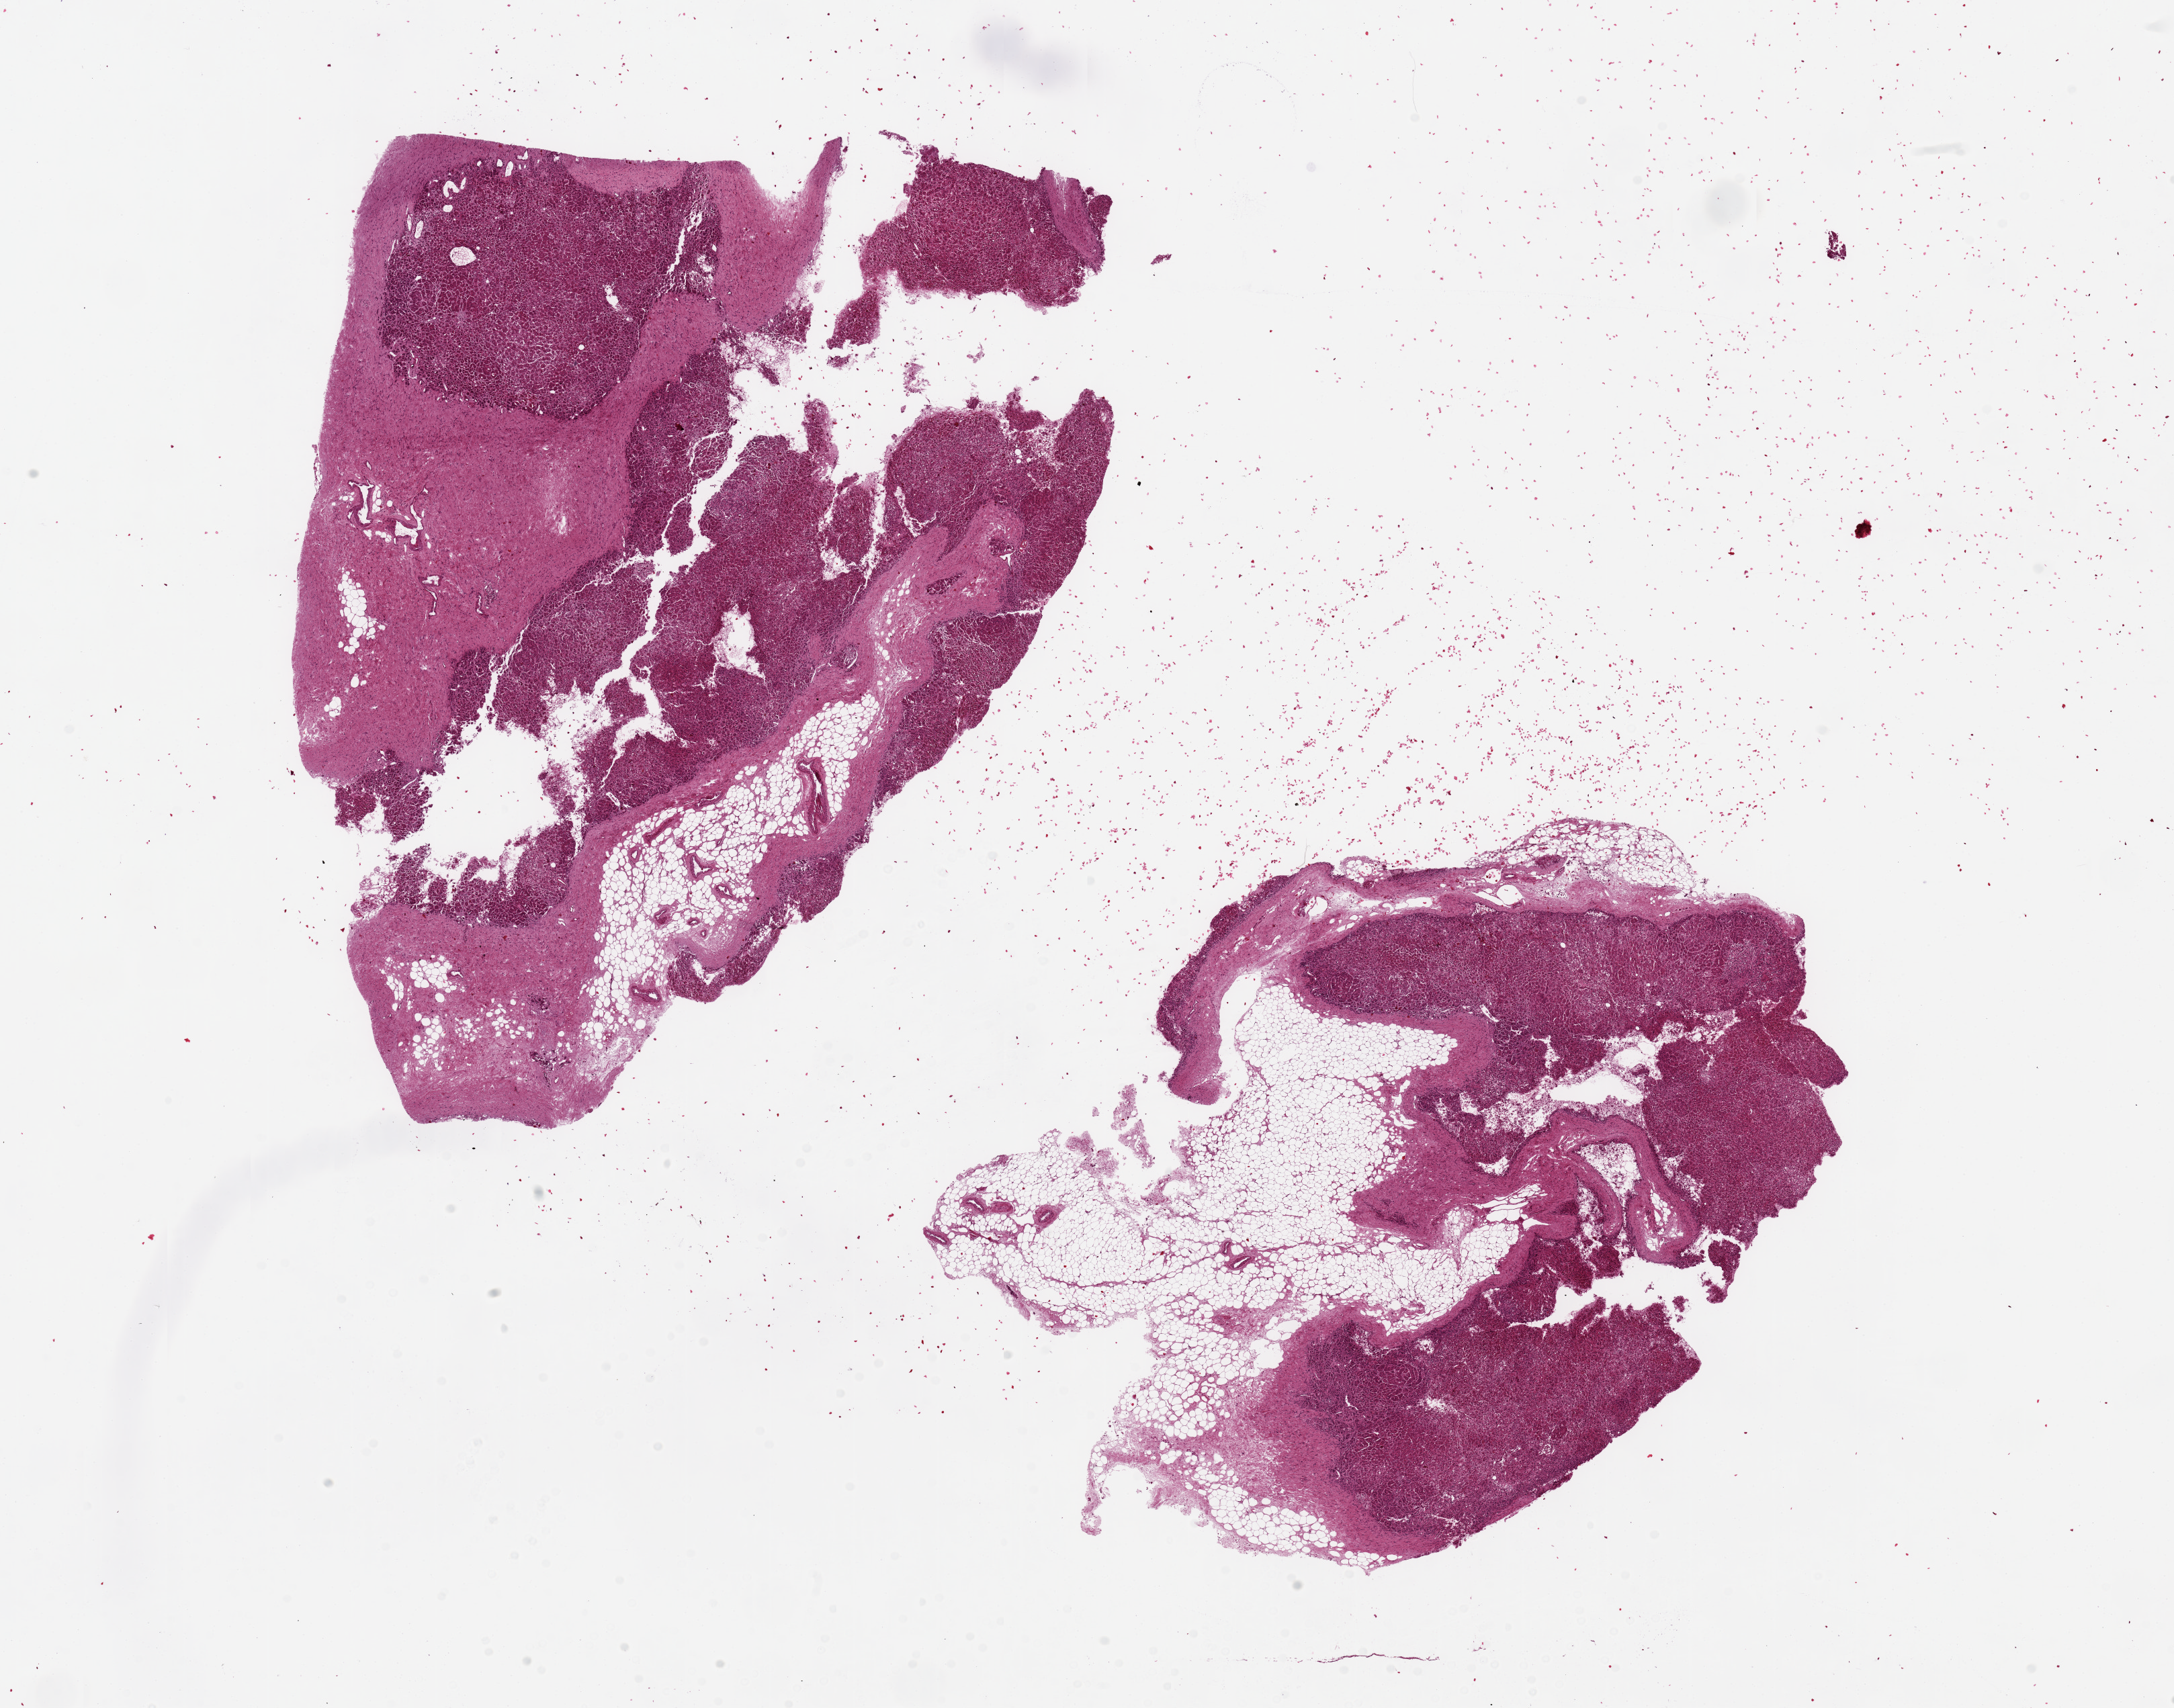
Digitized haematoxylin and eosin-stained section, brightfield — shown as a low-resolution overview of the whole scanned area (about 25.6 x 20.1 mm); PAXgene-fixed paraffin-embedded (PFPE) section; sampled site (target tissue): adrenal gland; donor tissue sample. Donor: male.
Reviewer comment on this tissue sample: 2 pieces ~10x9mm; 40% of each is cortex, 60% fat/fibrous tissue.